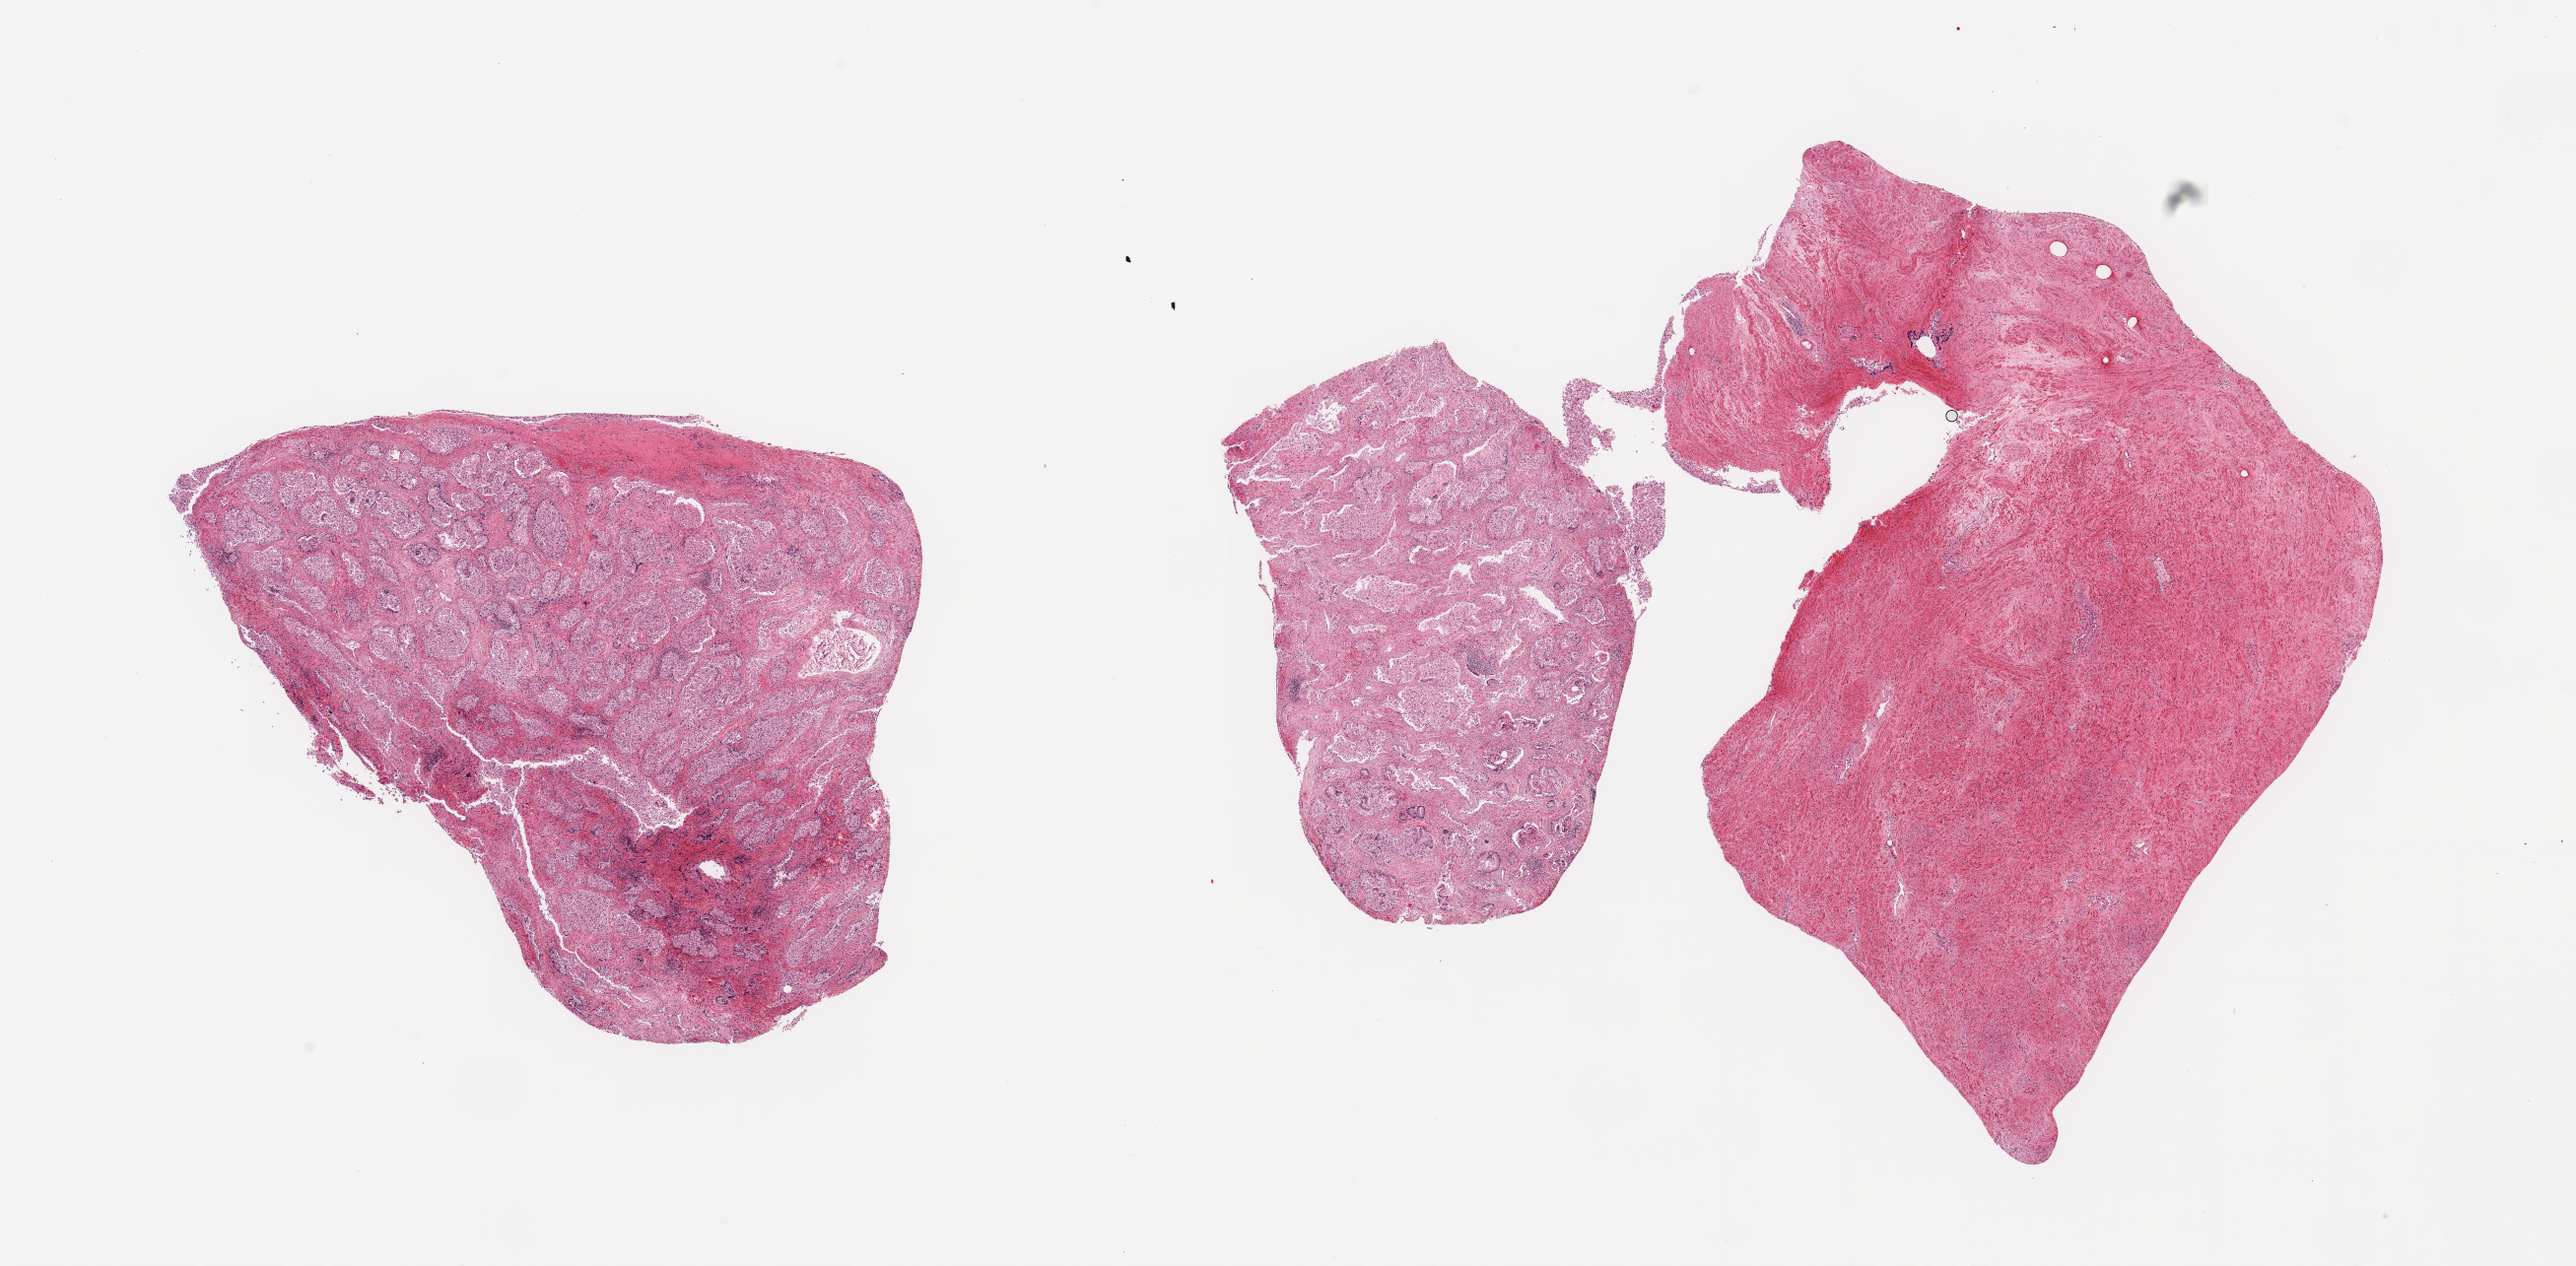
Whole-slide image, hematoxylin and eosin (H&E) stain, brightfield, shown as a low-resolution overview of the whole scanned area (about 20.7 x 10.2 mm, acquisition: 20x scan), PAXgene-fixed, paraffin-embedded tissue, target tissue: prostate, tissue donor sample.
- review note (as recorded): 3 pieces; two pieces of markedly autolyzed proliferating glandular component and one piece of fibromuscular stroma